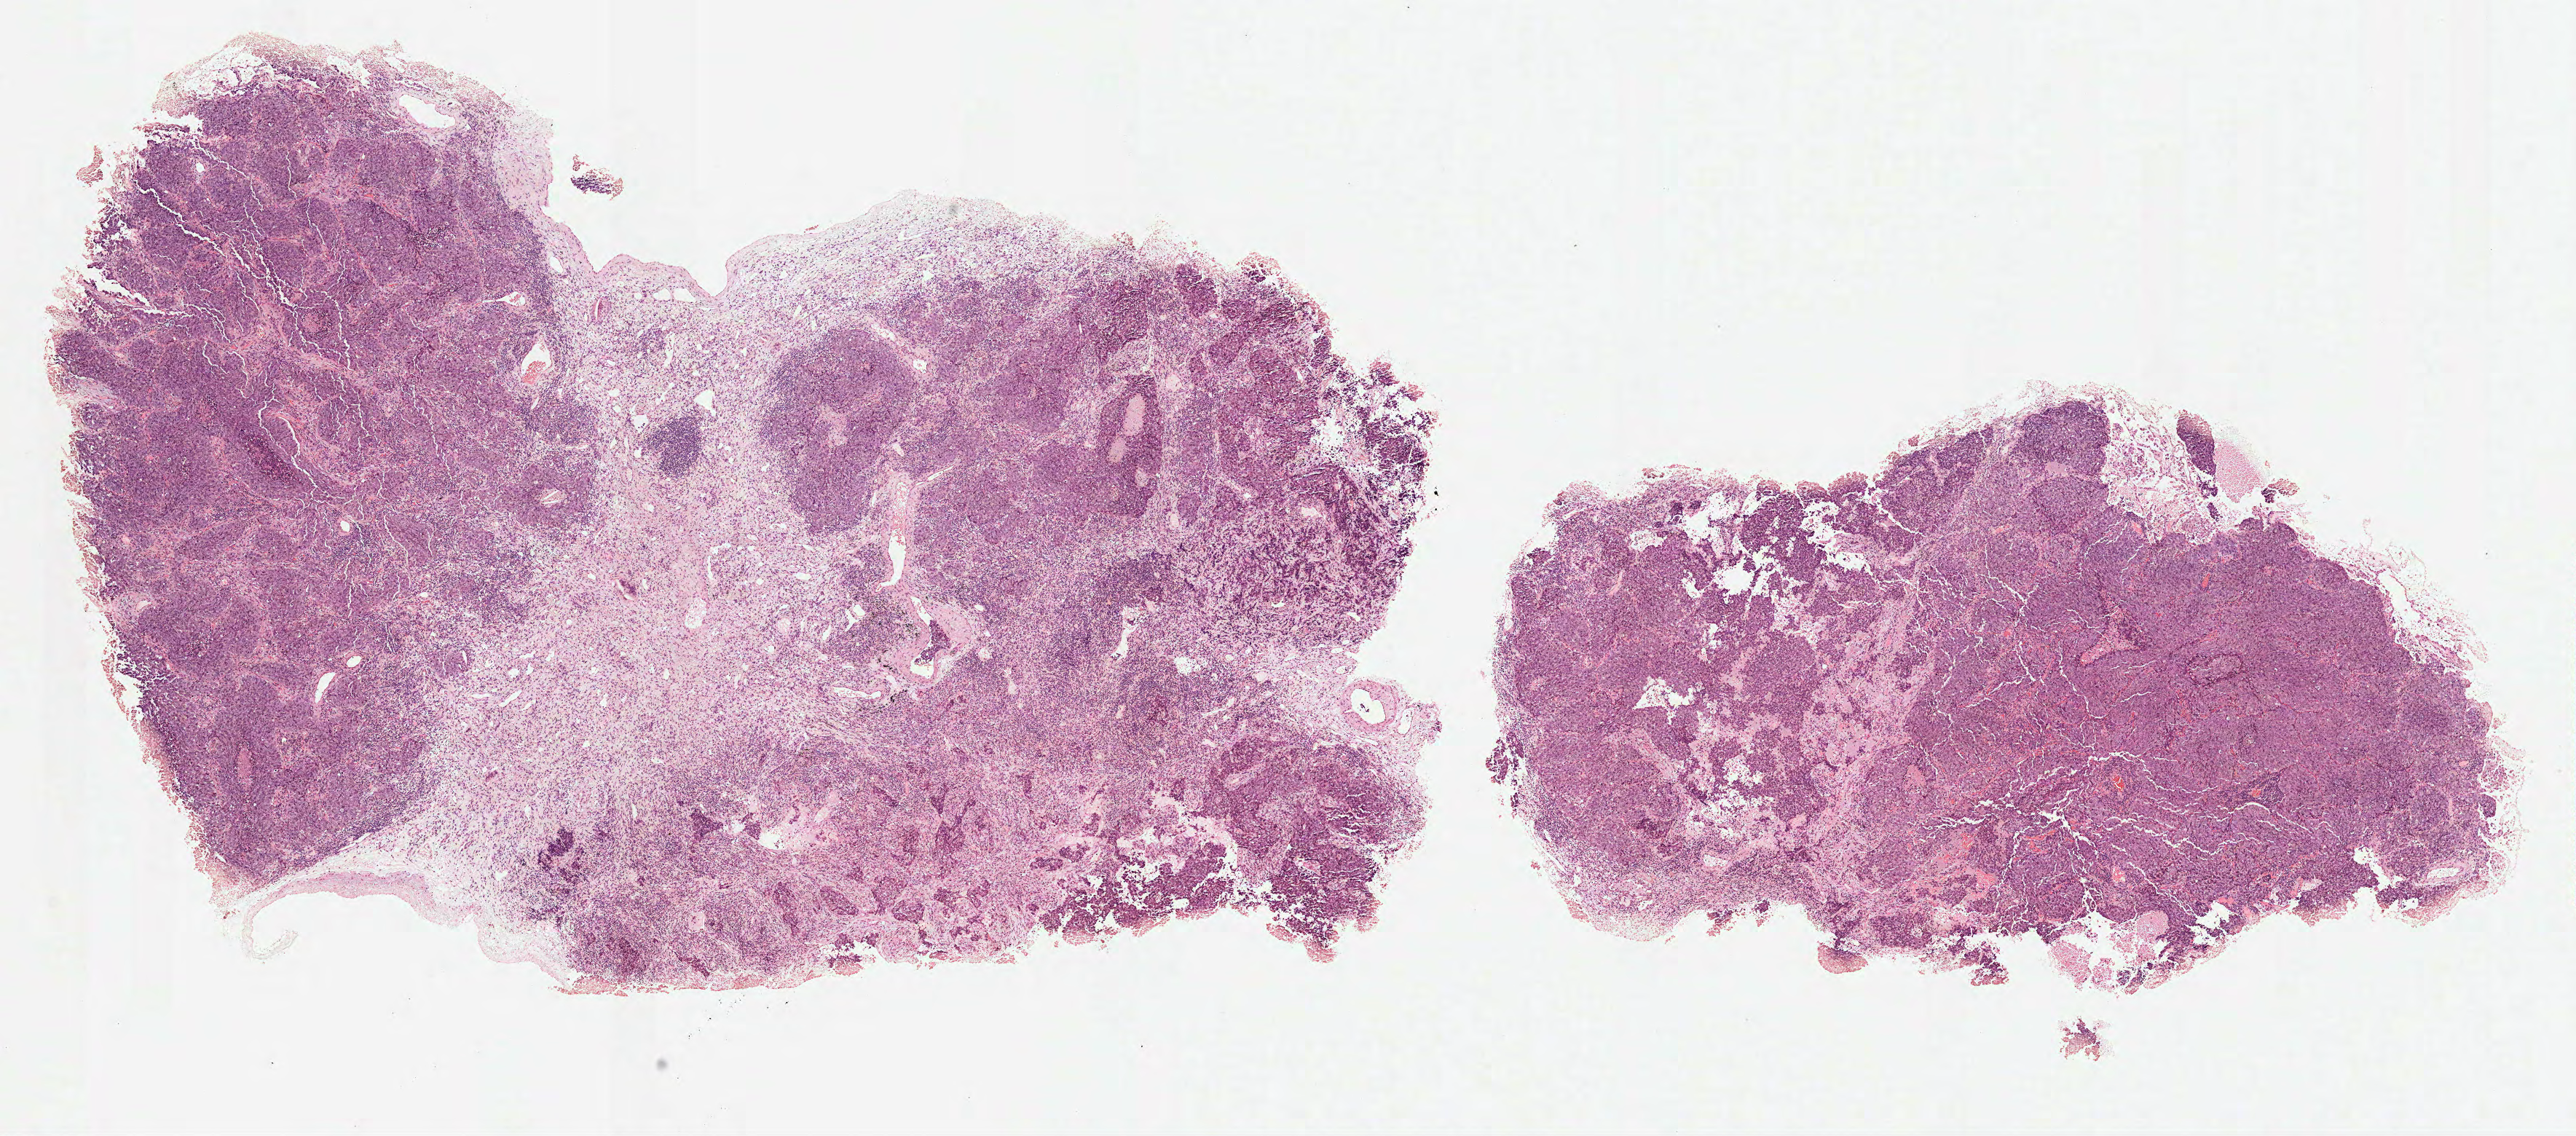
Digitized H&E tissue section (whole slide) — whole scanned area (about 14.3 x 6.3 mm, from a 40x scan) shown as a low-resolution overview. Formalin-fixed paraffin-embedded (FFPE) diagnostic section. Lung, primary tumour sample. Female patient; age at initial diagnosis 75 years.
Laterality: right. AJCC pathologic stage: IA. Histologic diagnosis: Squamous cell carcinoma, NOS.